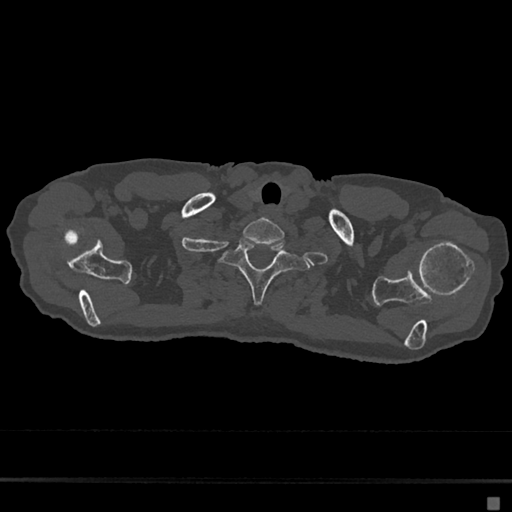
CT including the spine, one axial slice; slice 612 of 797 in the series (ordered by position); bone window (W 1800 / L 400 HU); 0.5 mm slice thickness; 512 × 512 image matrix, field of view 360 × 360 mm. Female patient, age 68 years. Case-level facts recorded for this patient, not image findings: primary cancer: renal.
Outlined on this slice (semi-automatic segmentation, software-assisted and operator-edited):
- T1 vertebra: bounding box (x1, y1, x2, y2) in pixels: (220, 238, 310, 305)